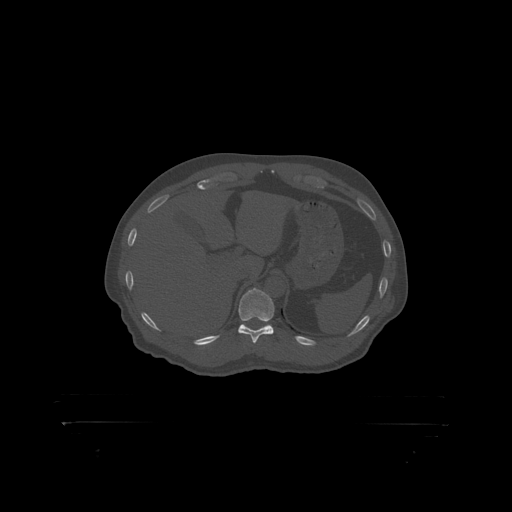
CT including the spine, one axial slice. Slice 375 of 399 in the series (ordered by position). 120 kVp. Bone window (W 1800 / L 400 HU). 1.25 mm slice thickness. 512 × 512 image matrix, field of view 650 × 650 mm. Male patient, age 46 years. Case-level facts recorded for this patient, not image findings: primary cancer: skin.
Annotated regions visible in this slice (semi-automatic segmentation, software-assisted and operator-edited):
- T11 vertebra: box from (x=239, y=288) to (x=275, y=319) px